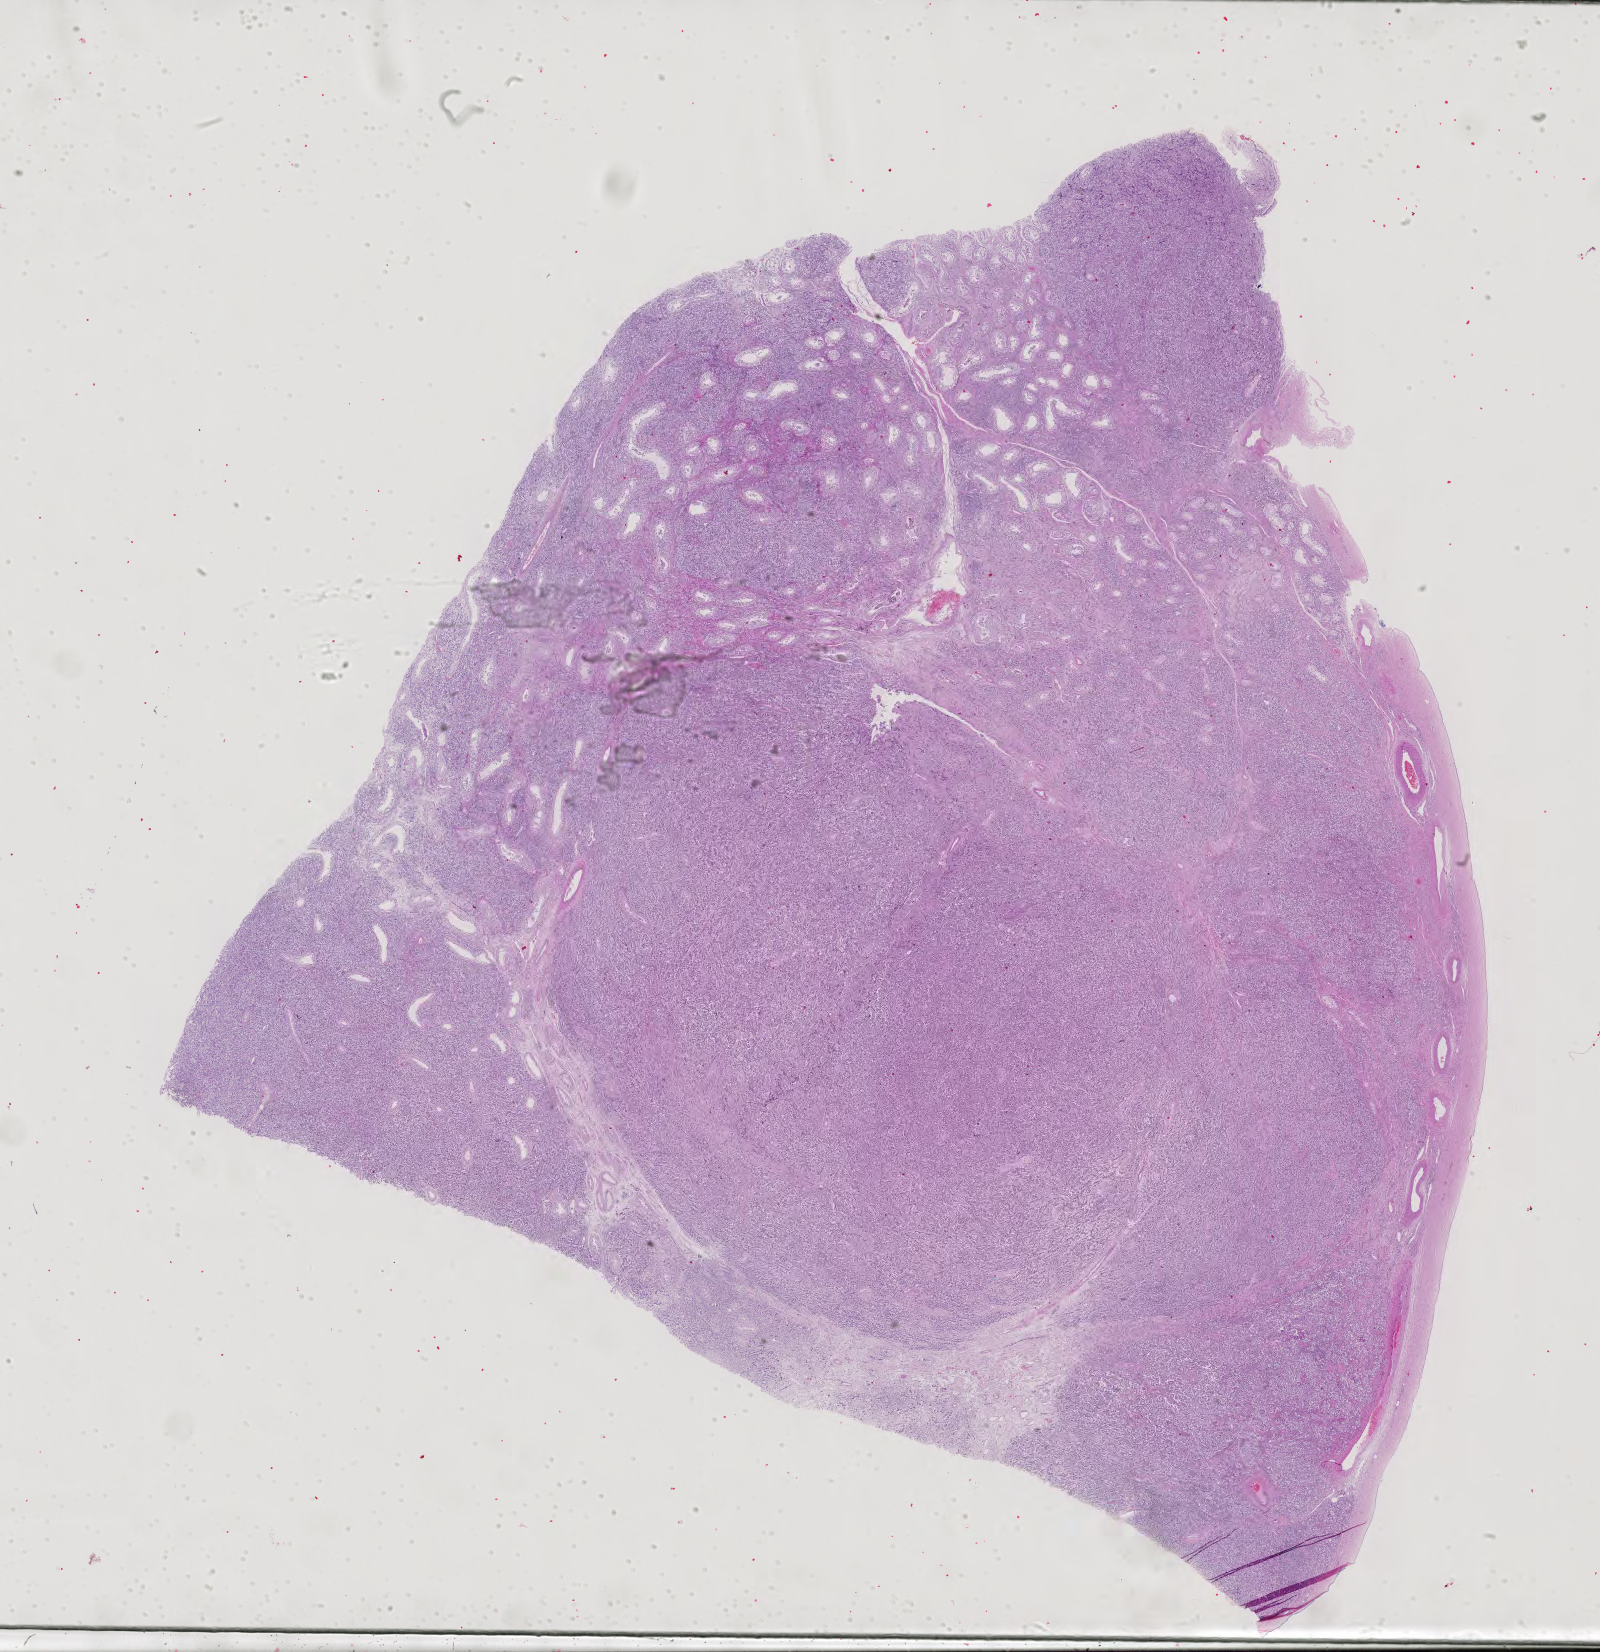
Digitized Hematoxylin and eosin (H&E) stained tissue section (whole slide) — whole scanned area (about 23.3 x 24.1 mm, slide scanned at 40x) shown as a low-resolution overview. Formalin-fixed paraffin-embedded (FFPE) diagnostic section. Testis, primary tumour sample. Male patient; age at initial diagnosis 37 years.
Pathologic diagnosis: Seminoma, NOS.